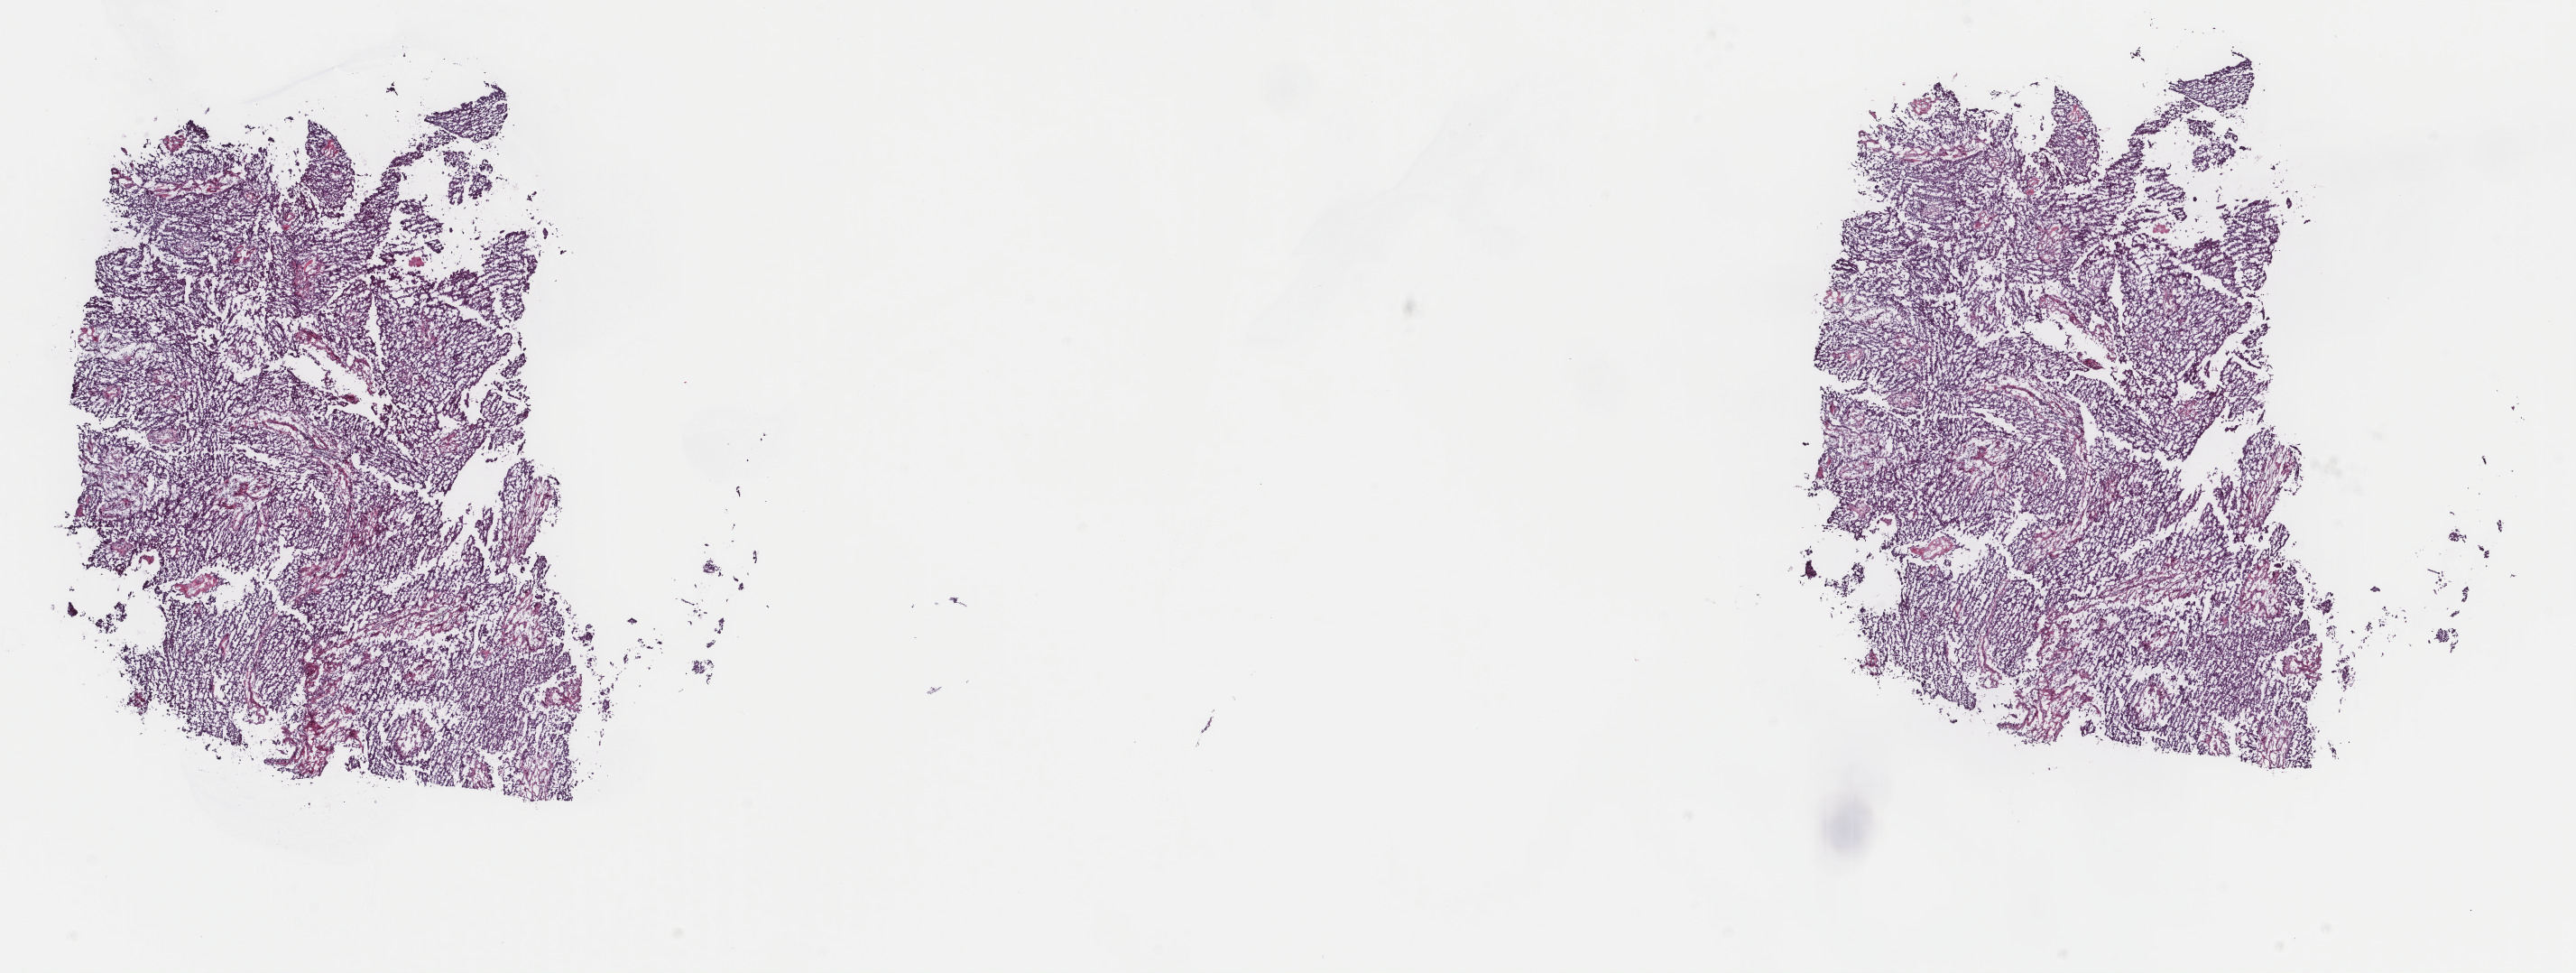
Whole-slide histology image, H&E-stained — low-resolution overview of the scanned area, about 22.7 x 8.6 mm (from a 40x scan). Frozen section. Primary tumour sample from the bladder. Patient: male, age at initial diagnosis 62 years. Histologic grade: low grade. Composition of this section per pathologist review: tumour cells 90%, tumour nuclei 90%, normal cells 0%, stromal cells 10%, necrosis 0%. Infiltration values recorded for this section: lymphocyte infiltration 2%, monocyte infiltration 1%, neutrophil infiltration 1%.
* AJCC pathologic stage: II
* histologic diagnosis: Papillary transitional cell carcinoma
* TNM: T2 N0 M0